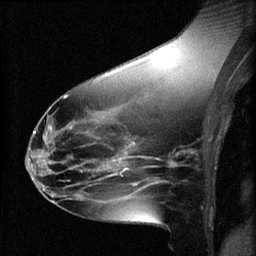
Breast MRI (dynamic contrast-enhanced), one sagittal slice. Position 29 of 60 along the scan axis. 3 images stored at this slice position (order not interpretable as contrast timing). 1.5 T. TE 4.2 ms, TR 8.2 ms. 2 mm slice thickness. 256 × 256 image matrix, field of view 180 × 180 mm. Female patient, age 49 years.
Outlined on this slice (semi-automatically segmented with operator editing):
- analysis volume of interest (the breast-tissue region the enhancement analysis was run in; not a lesion): bounding box [x1, y1, x2, y2] px = [45, 136, 109, 187]
- tumour enhancement mask (voxels above the 70 % enhancement threshold inside the analysis volume of interest): [77, 166, 108, 169]